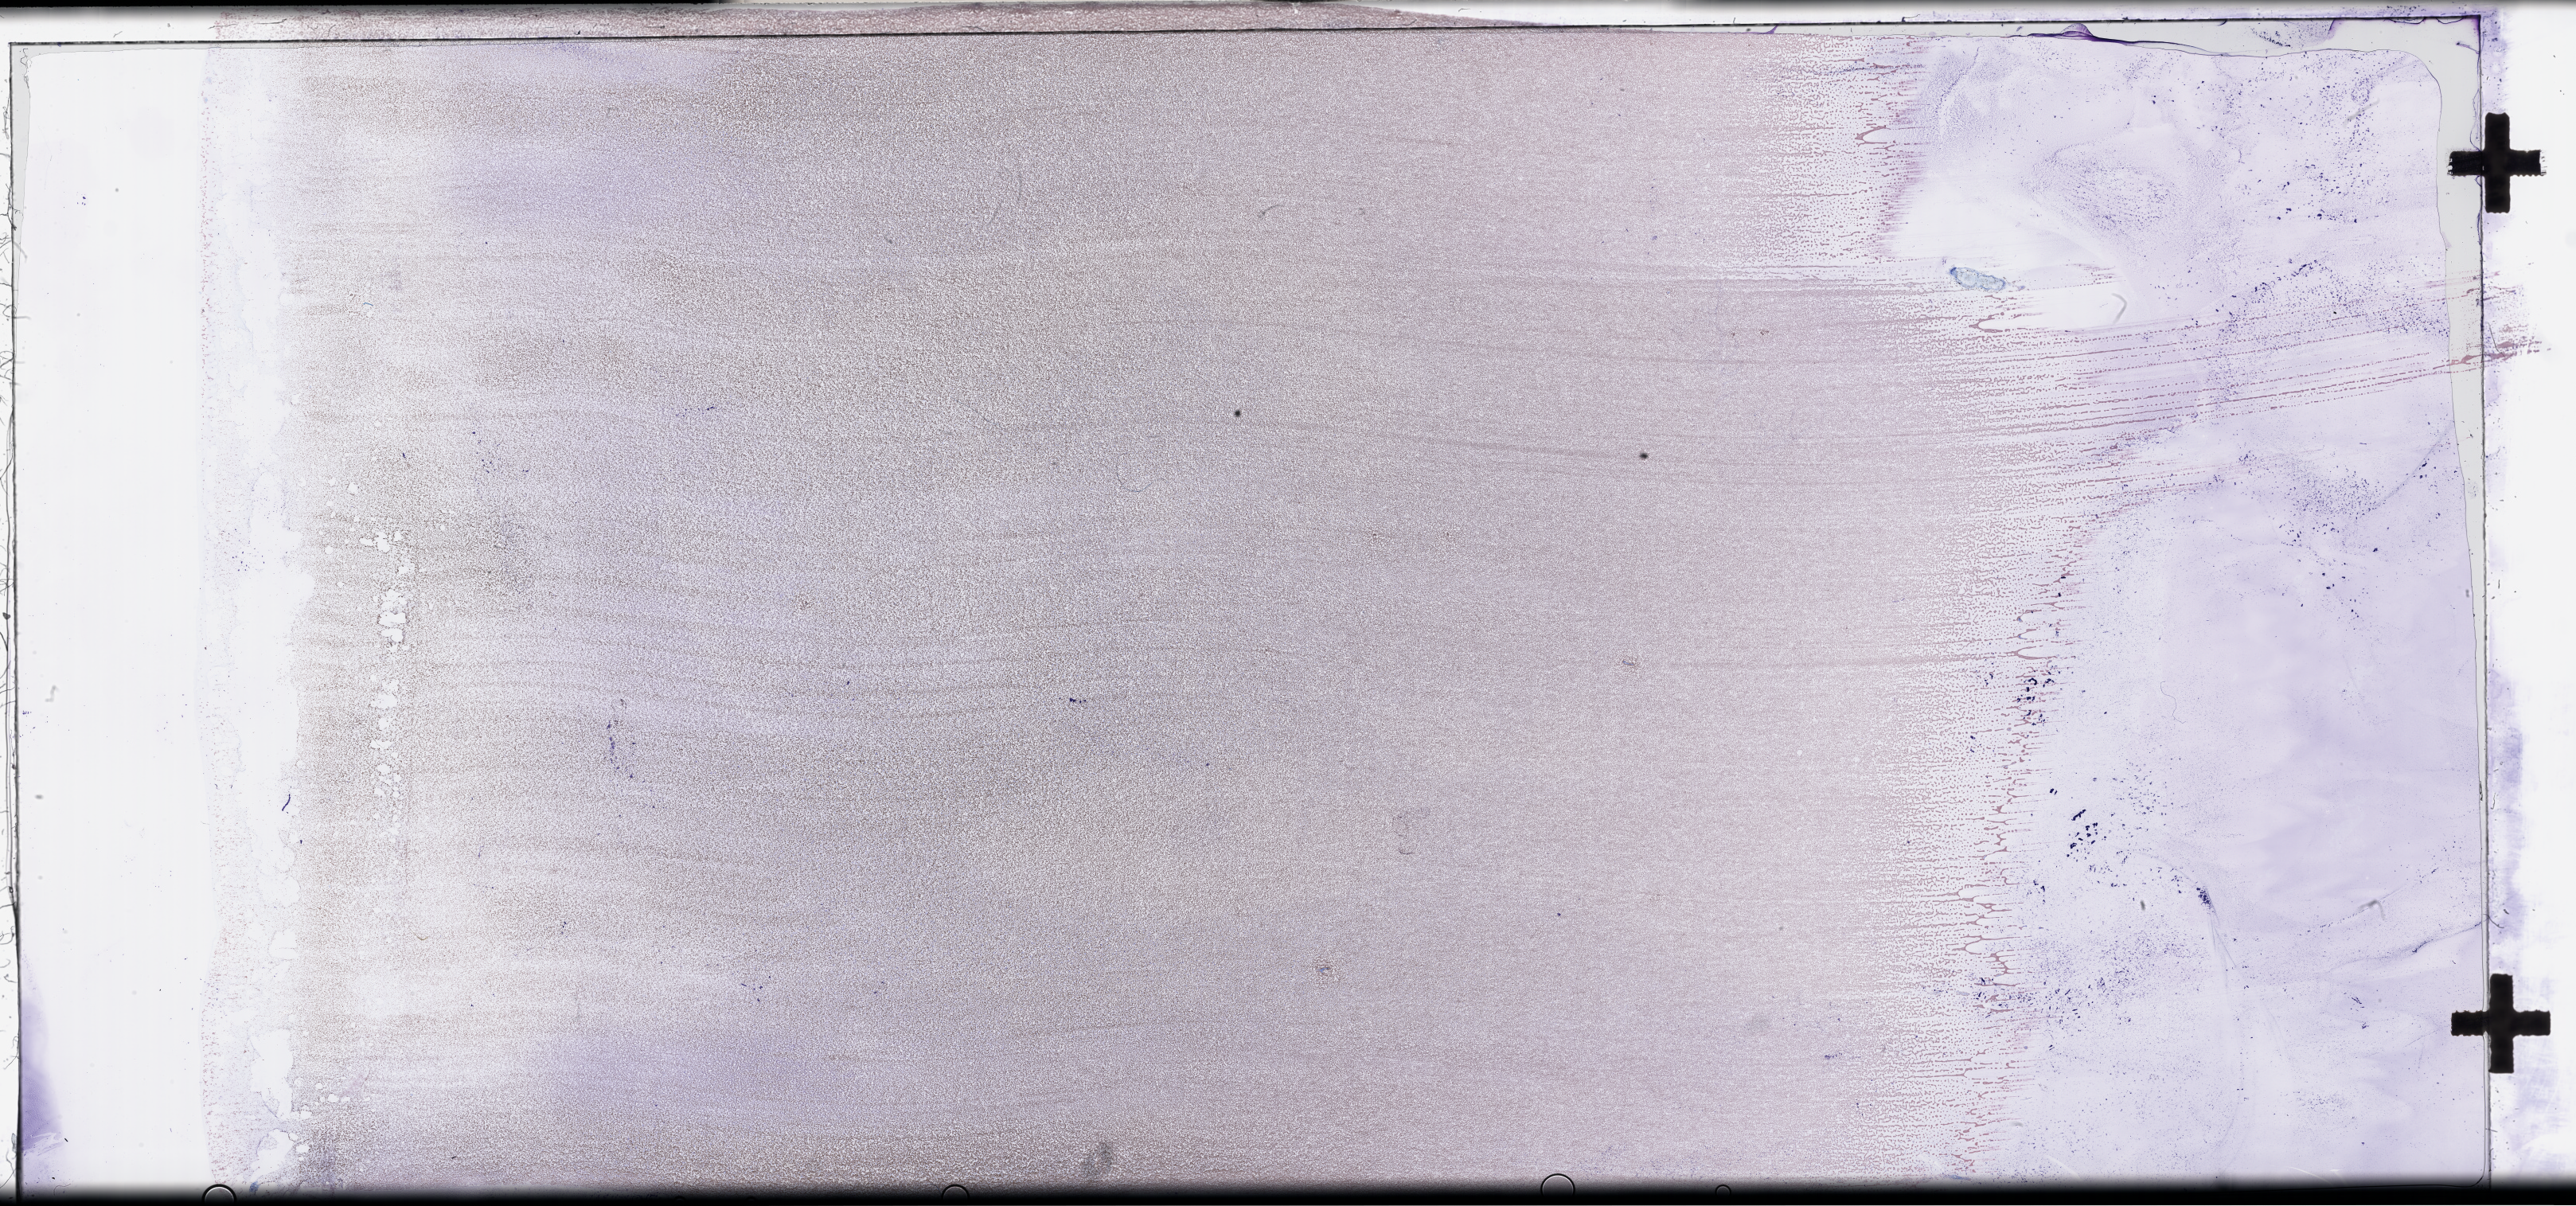
Whole-slide image of a whole blood smear, Wright-Giemsa stain — a low-resolution overview of the entire scanned area, about 52.3 x 24.5 mm. Patient: female.
Patient diagnosis: Acute Myeloid Leukemia Not Otherwise Specified.